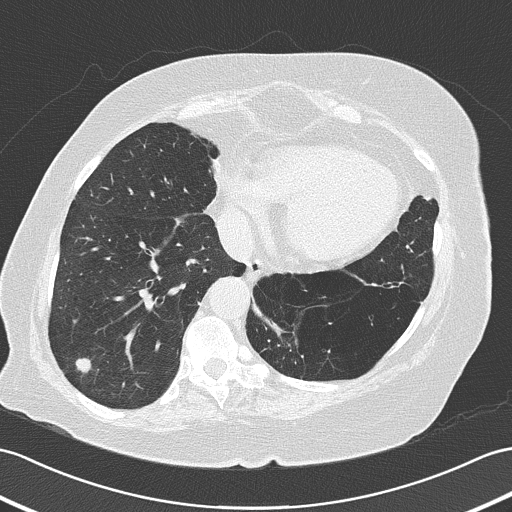
Chest CT (low-dose screening protocol), one axial image, baseline annual screen, lung window (W 1500 / L -600 HU), 2 mm slice thickness, slice 104 of 161 in the series, 512 × 512 image matrix. Female, age 73 years at enrolment.
• Lesion marked by an expert reader, box from (x=53, y=336) to (x=101, y=384) px.
• The screening reader recorded 4 non-calcified nodules or masses ≥4 mm on this exam (right lower lobe, right upper lobe, left upper lobe, left lower lobe); which of them this box marks is not recorded.
• Lung cancer was diagnosed 50 days after this screen: adenocarcinoma, NOS, right lower lobe, poorly differentiated (G3), stage IB (AJCC 6th edition), 17 mm at pathology.